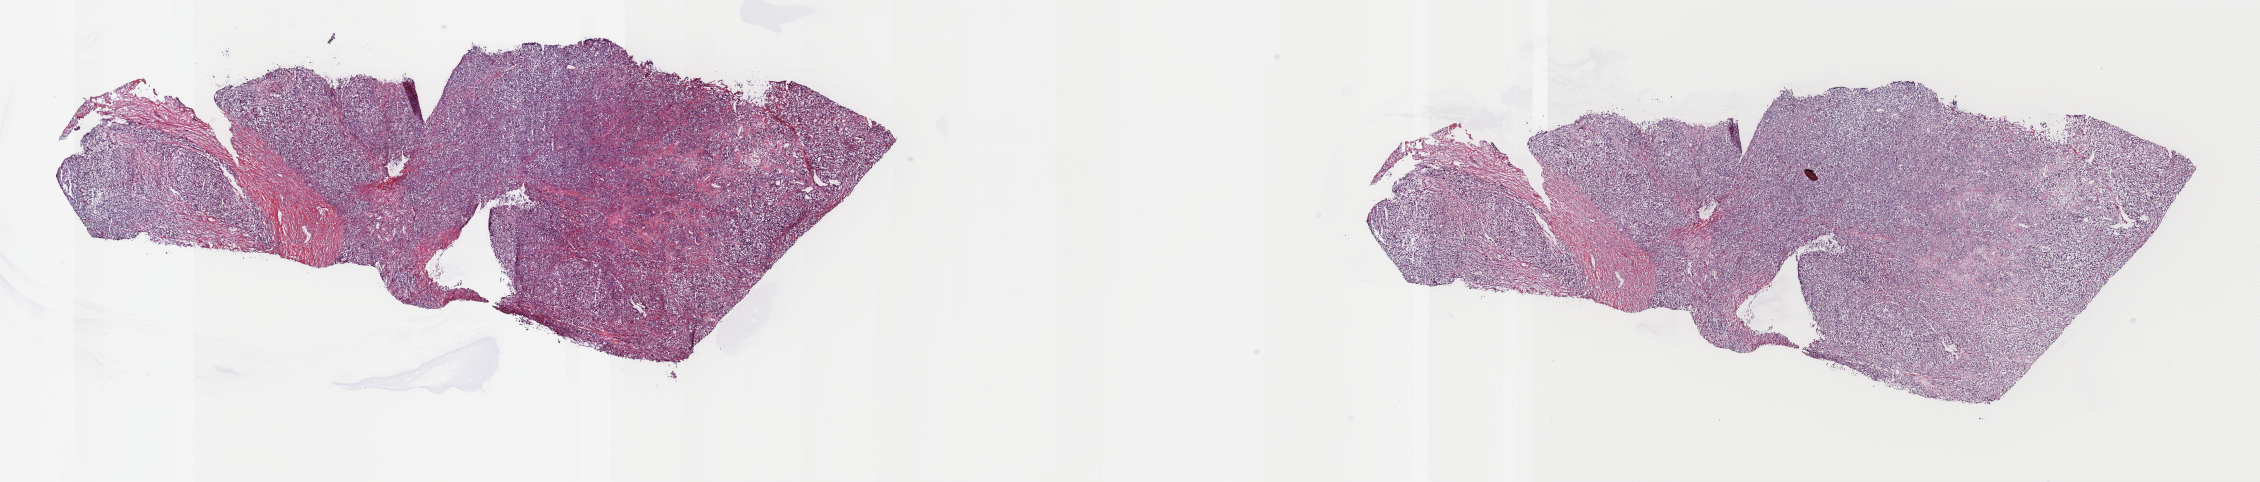
Whole-slide histology image, Hematoxylin and eosin (H&E) stained — shown as a low-resolution overview of the whole scanned area (about 35.9 x 7.7 mm), frozen section from the top of the tissue portion, metastatic tumour sample, sampled site: connective, subcutaneous and other soft tissues of upper limb and shoulder. Patient: female, age at initial diagnosis 60 years. Pathologist review of this section (percent, as recorded): tumour cells 90%, tumour nuclei 95%, normal cells 0%, stromal cells 10%, necrosis 0%. Inflammatory infiltration, as recorded: lymphocyte infiltration 1%, monocyte infiltration 0%, neutrophil infiltration 0%.
This section: metastatic tumour tissue. Patient diagnosis: Malignant melanoma, NOS.